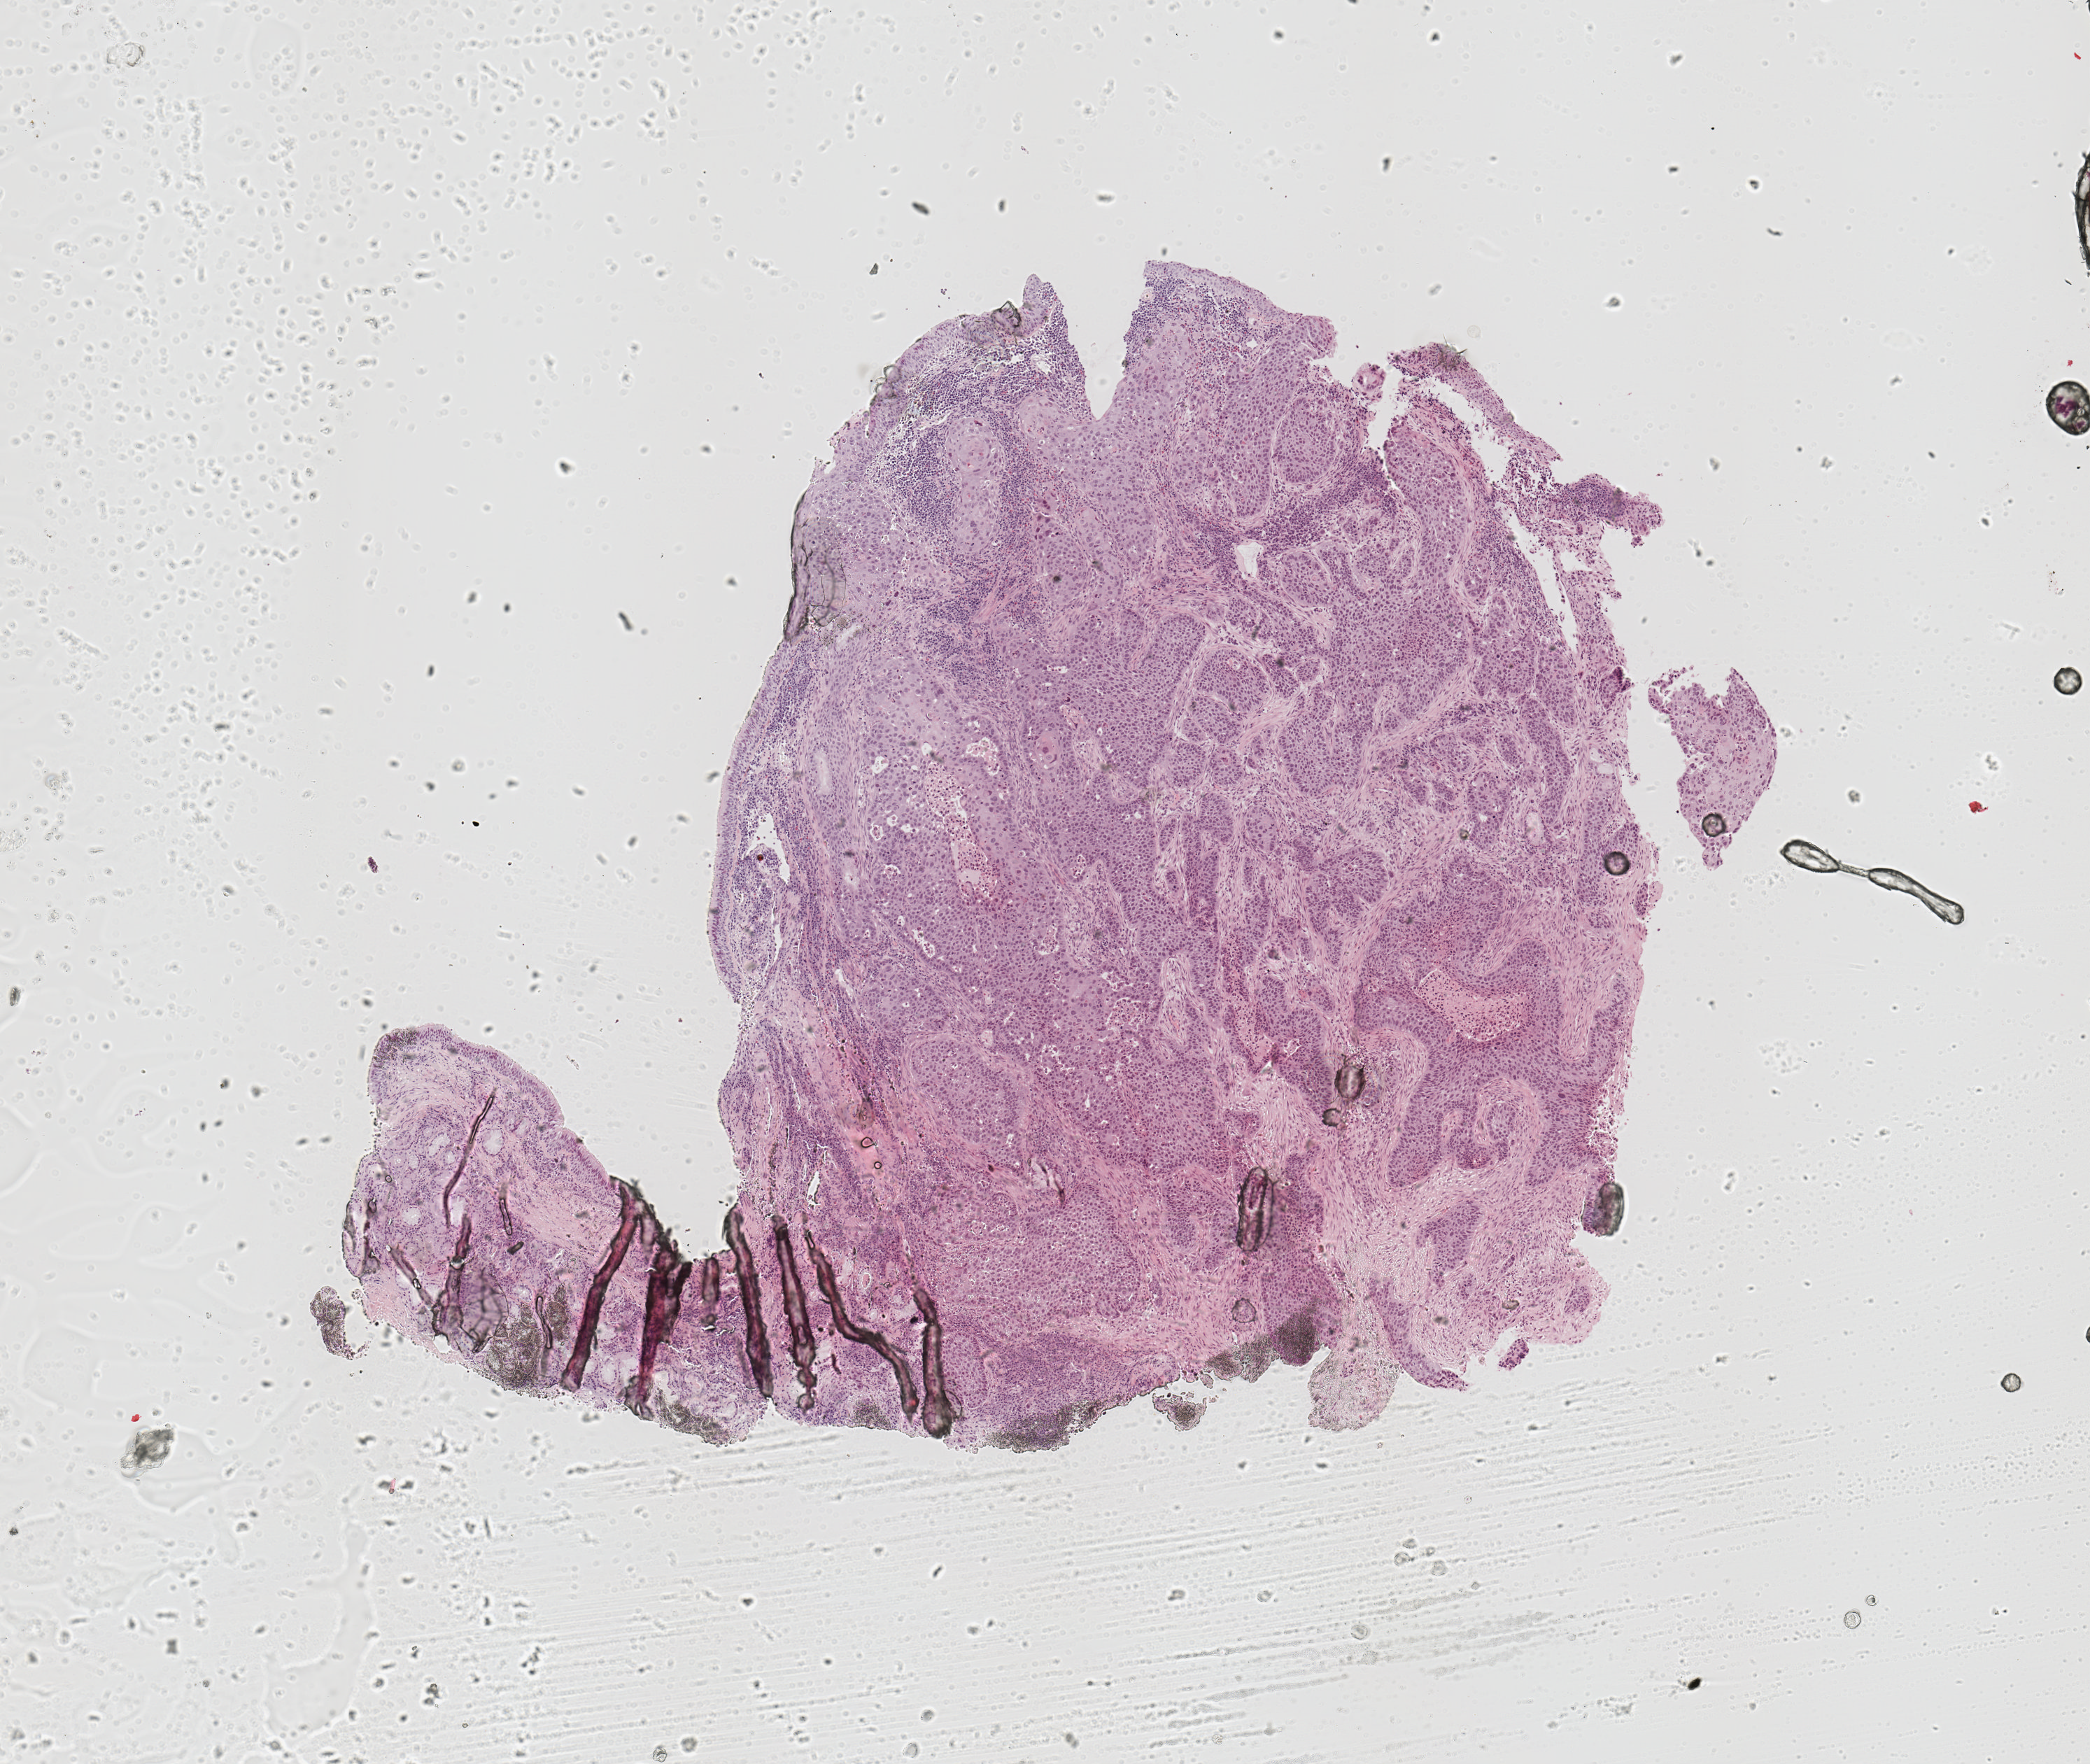
Digitized H&E-stained tissue section (whole slide) — low-resolution overview of the scanned area, about 5.9 x 5.0 mm (from a 20x scan); tumour tissue sample, sampled site: lung. 62-year-old male patient. Histologic grade: G3 (poorly differentiated). Composition of this section per pathologist review: tumour nuclei 70%, necrosis 5%.
AJCC pathologic stage: IIIA. Primary tumour site (as recorded): right upper lobe. Diagnosis: Squamous cell carcinoma, NOS.